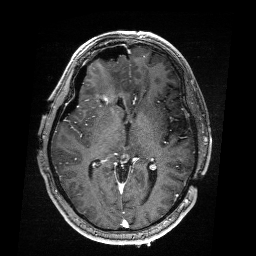
Brain MRI from a brain-tumour surgery series, one axial slice. Slice 107 of 176 in the series (ordered by position). T1-weighted post-contrast. 1 mm slice thickness. 256 × 256 image matrix, field of view 256 × 256 mm. From the clinical record (not read from this slice): histopathology: Astrocytoma; WHO grade: 4; IDH mutation: yes; tumour location: Right Frontal.
Annotated regions visible in this slice (outlined manually by an expert reader):
- residual tumour: bounding box [x1, y1, x2, y2] px = [91, 89, 105, 97]